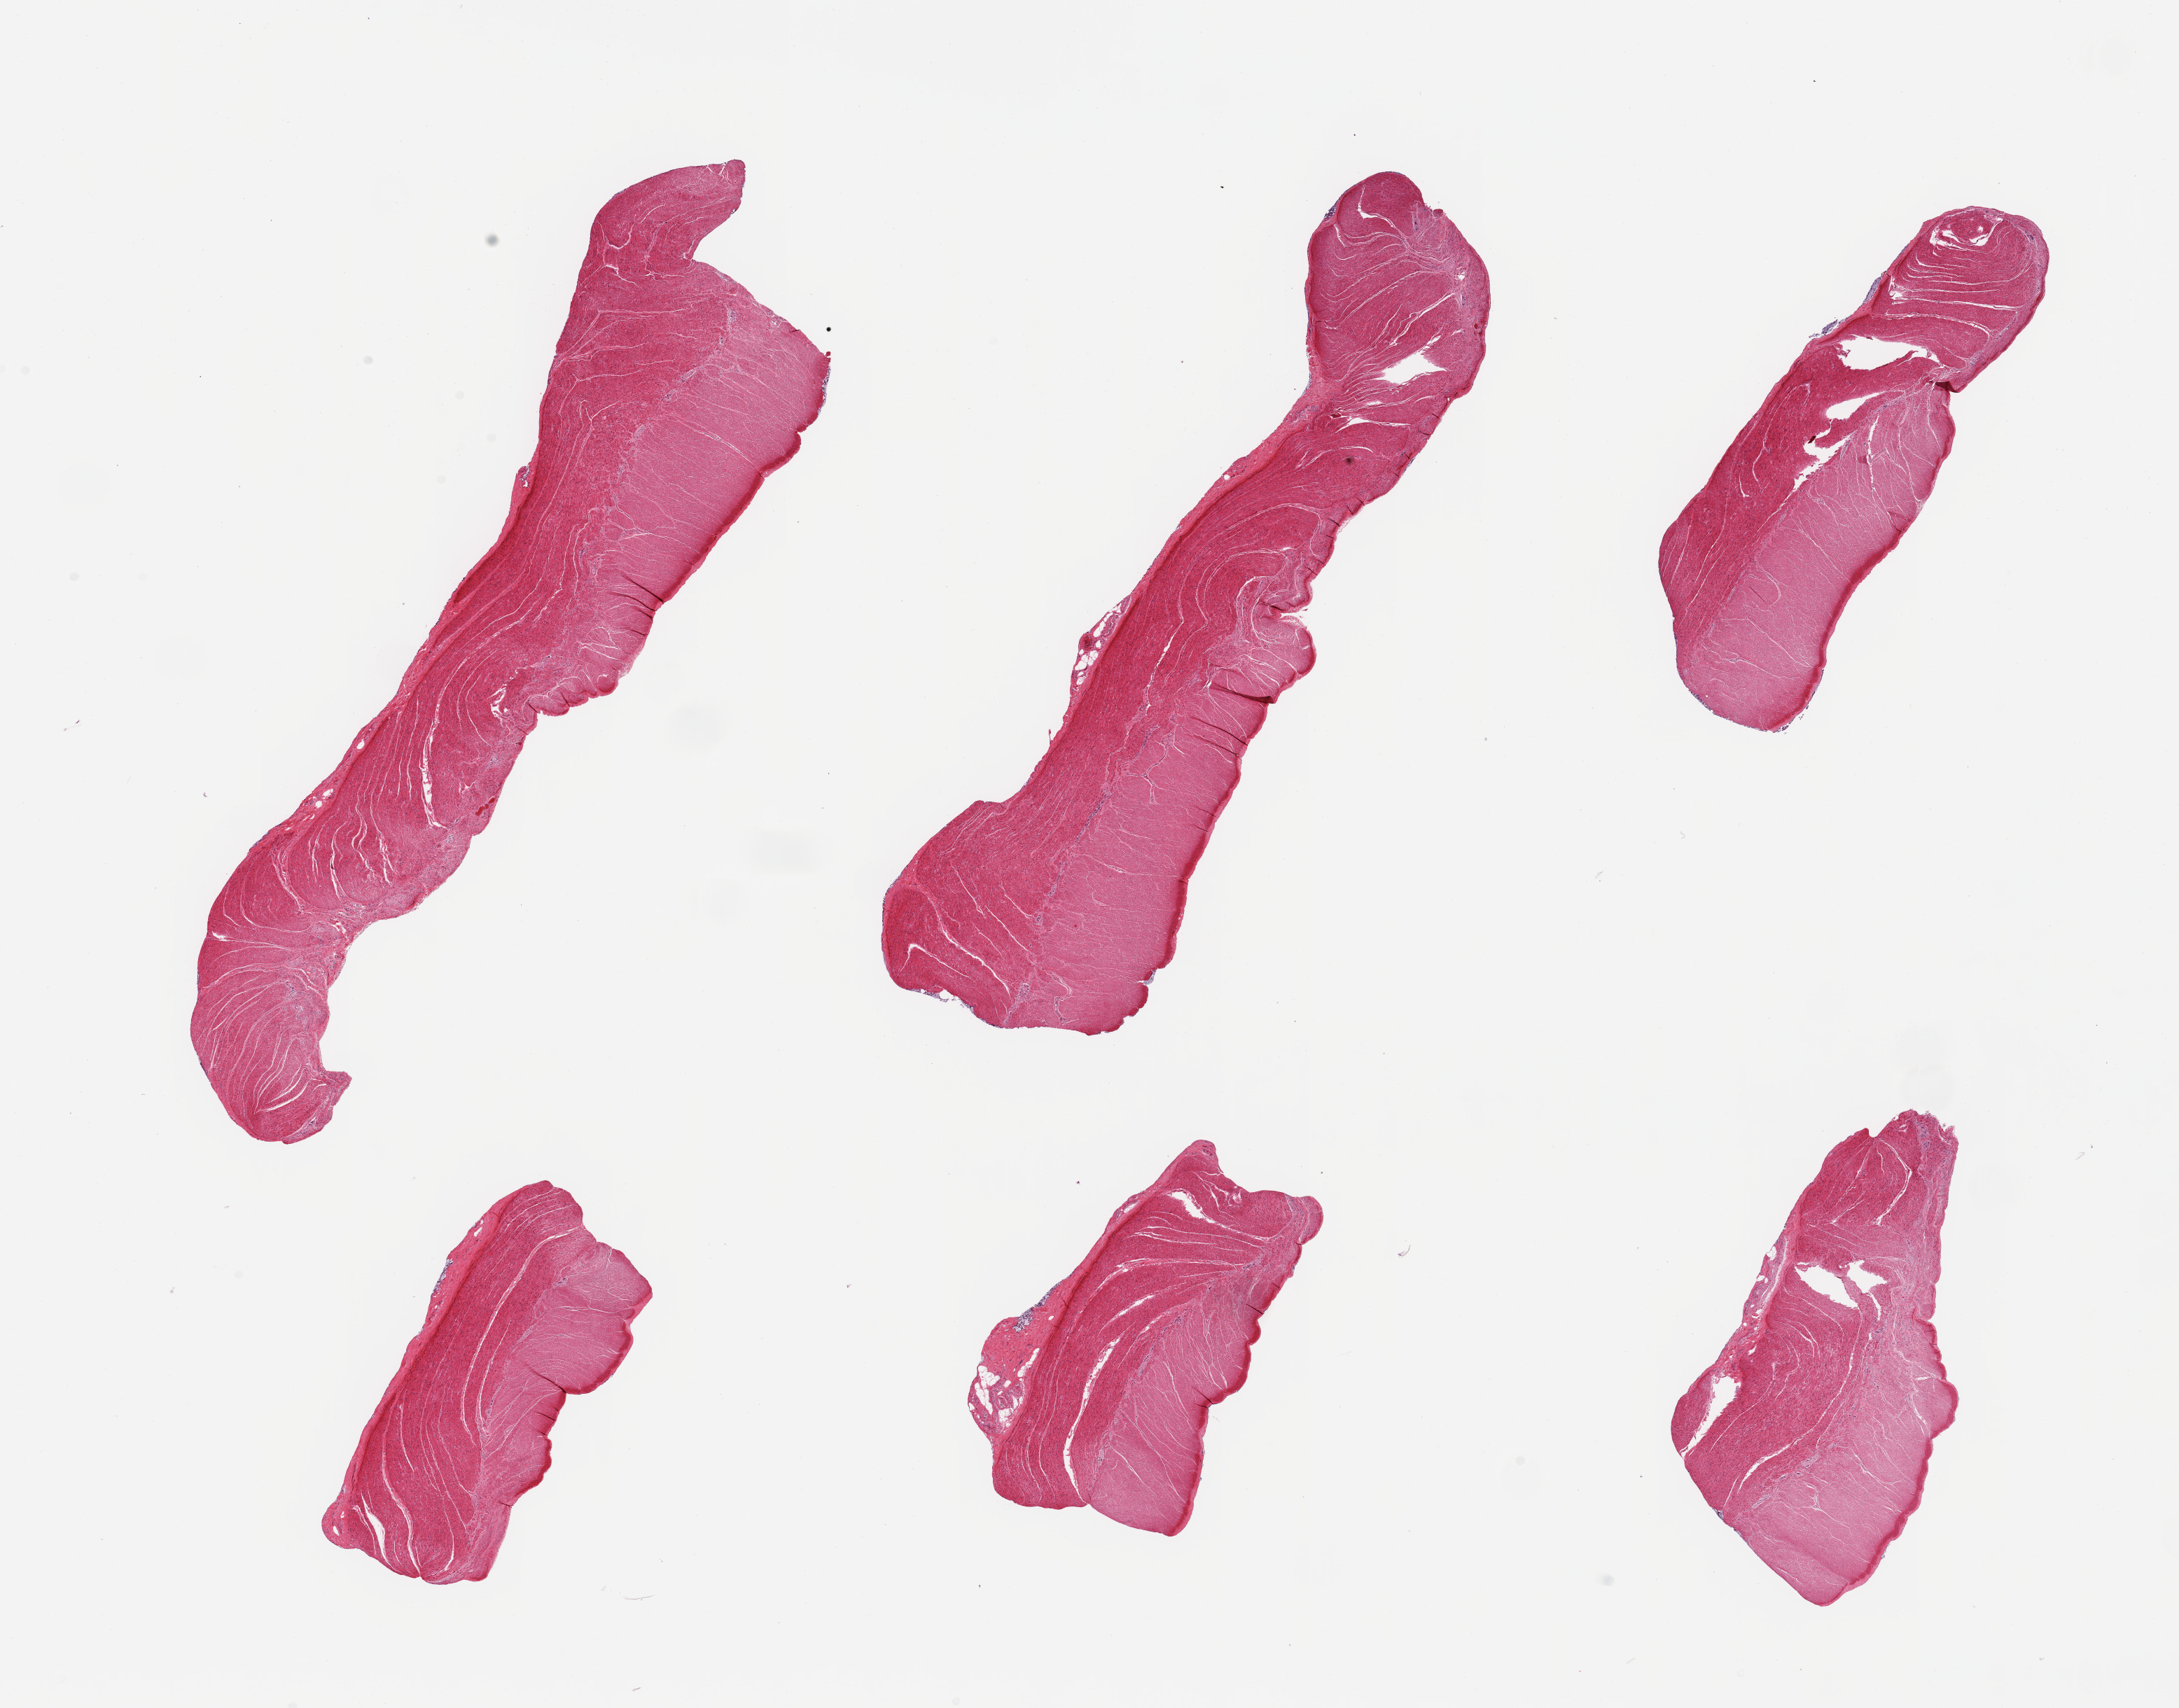
Digitized haematoxylin and eosin-stained section — shown as a low-resolution overview of the whole scanned area (about 24.6 x 19.3 mm); PAXgene-fixed paraffin-embedded (PFPE) section; sampled site (target tissue): sigmoid colon; tissue donor sample. Donor sex: male.
- pathologist's review note for this sample: 6 pieces; well trimmed target muscularis